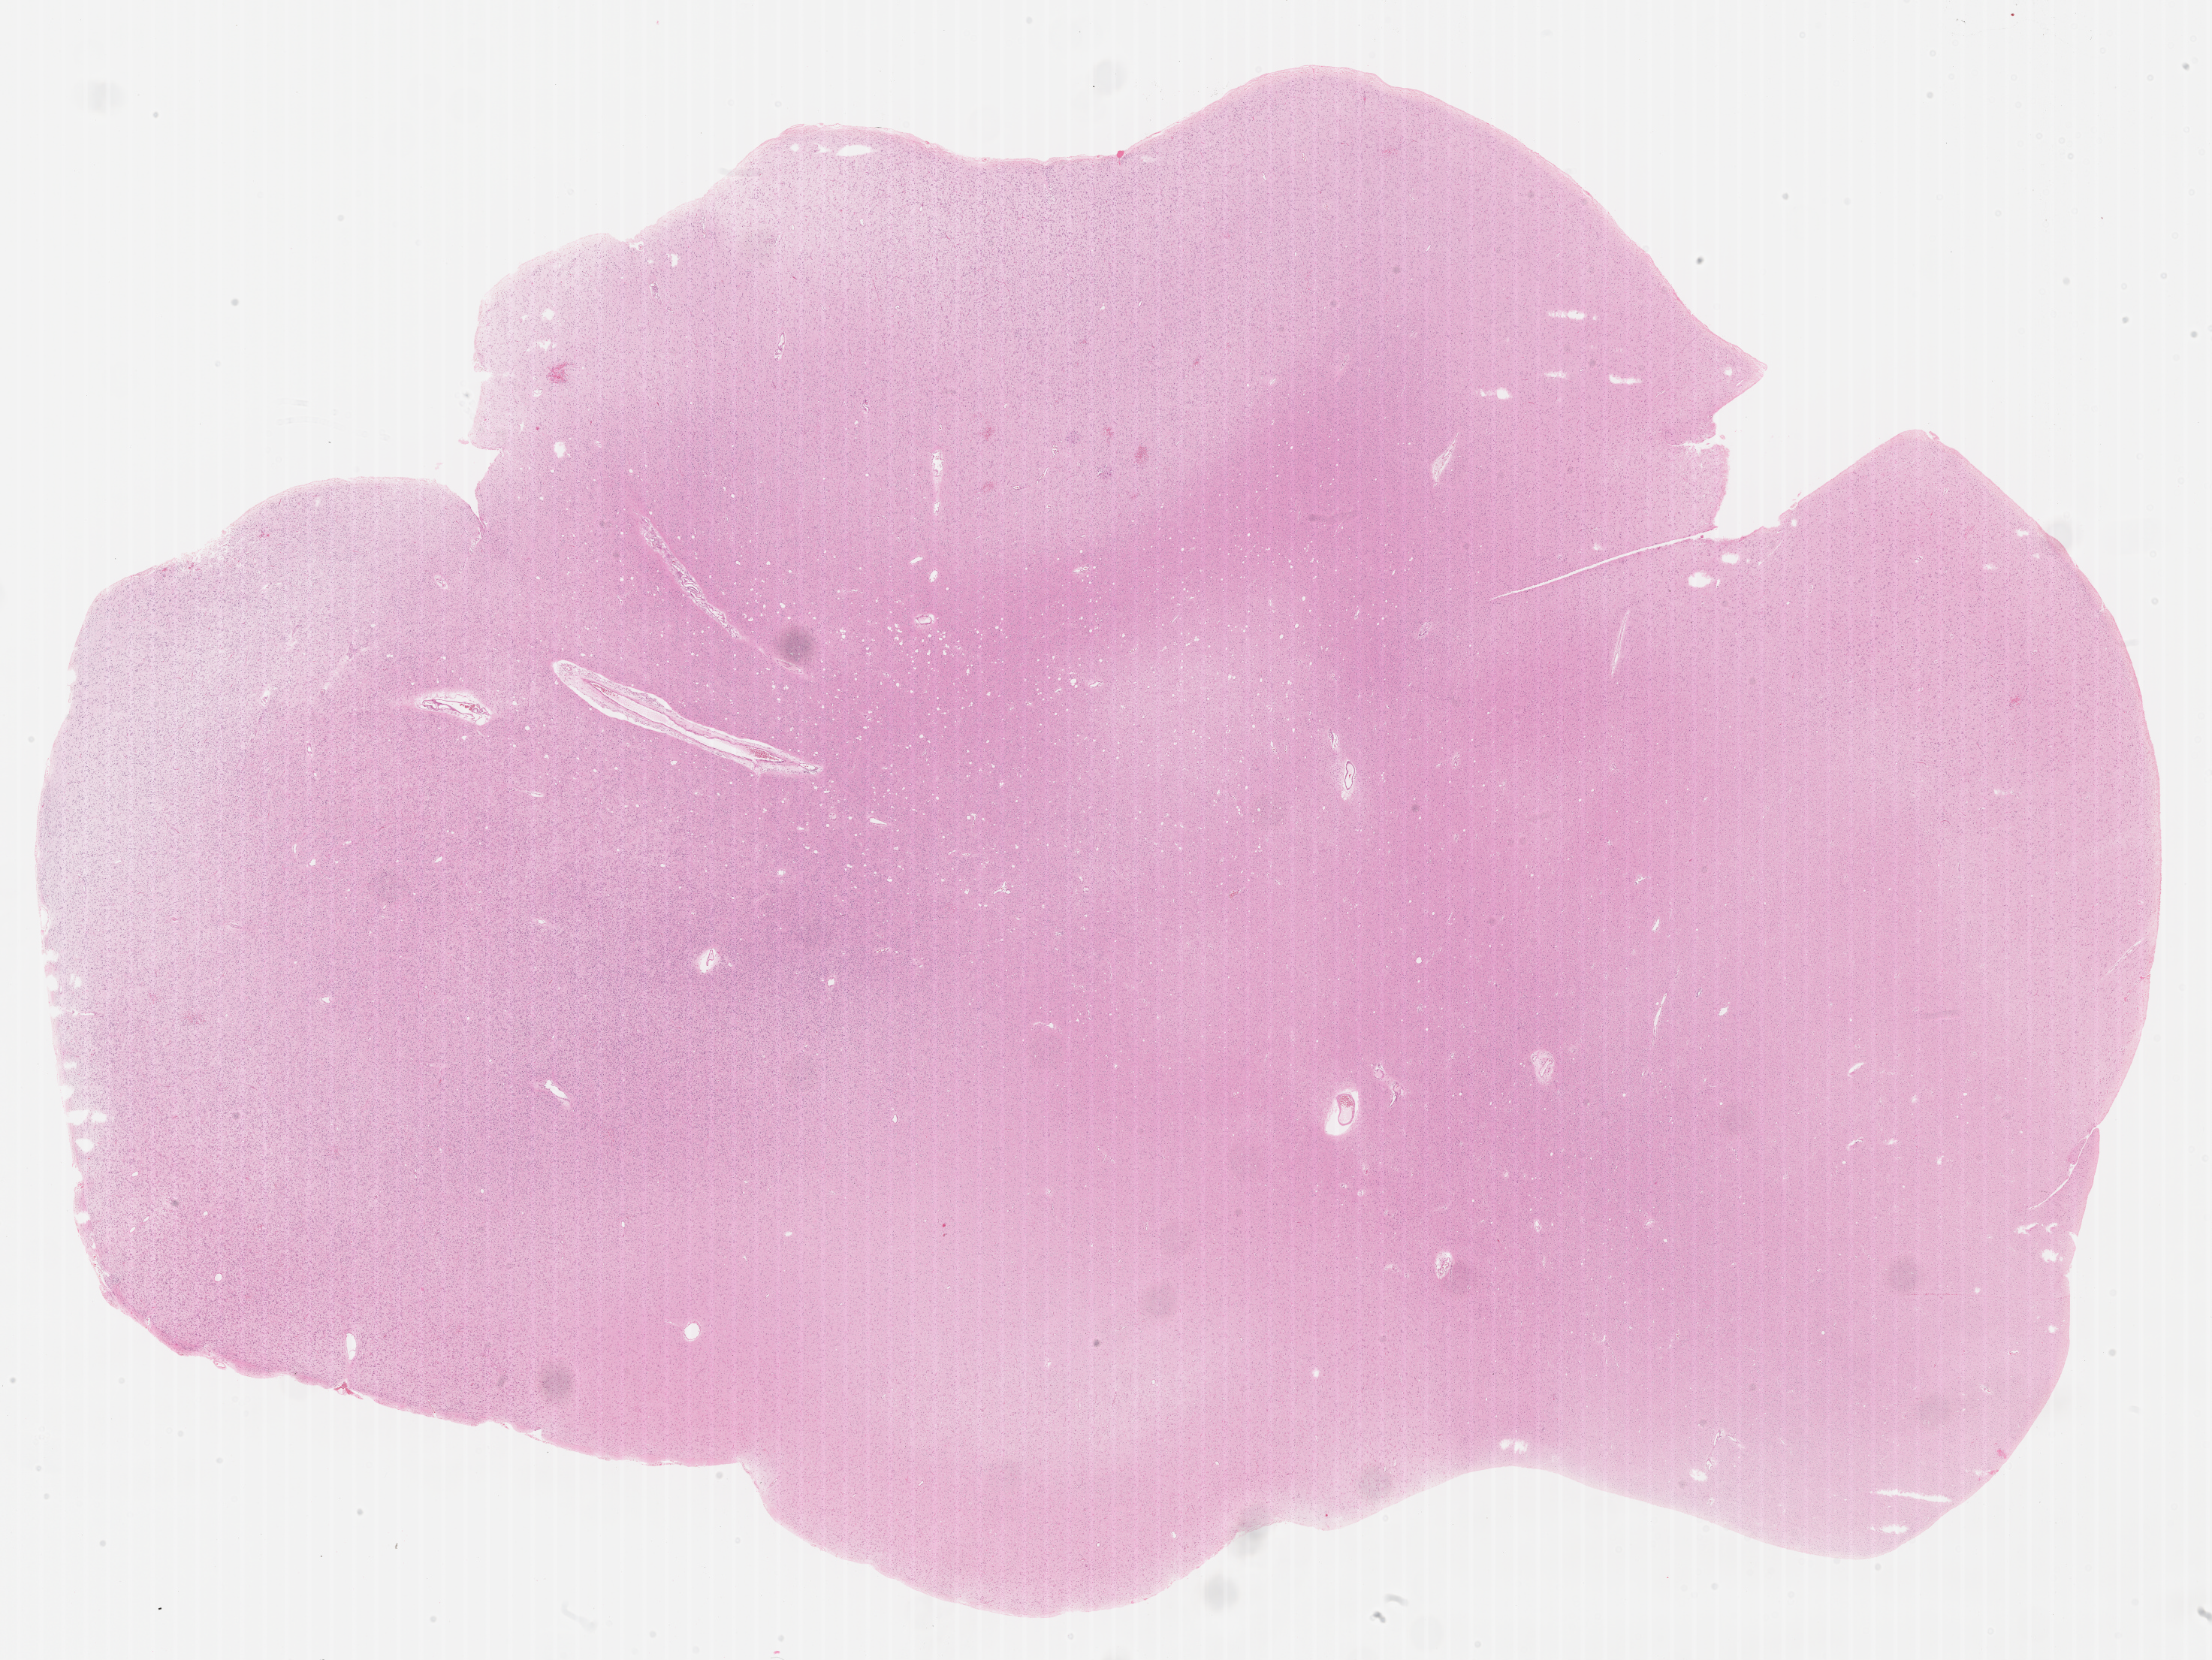
Whole-slide histology image, H&E-stained, whole scanned area (about 23.7 x 17.8 mm, acquisition: 40x scan) shown as a low-resolution overview; formalin-fixed paraffin-embedded (FFPE) diagnostic section; brain, primary tumour sample. Patient: male, age at initial diagnosis 40 years. Histologic grade: G2 (moderately differentiated).
Laterality: right. Pathologic diagnosis: Oligodendroglioma, NOS (cerebrum).